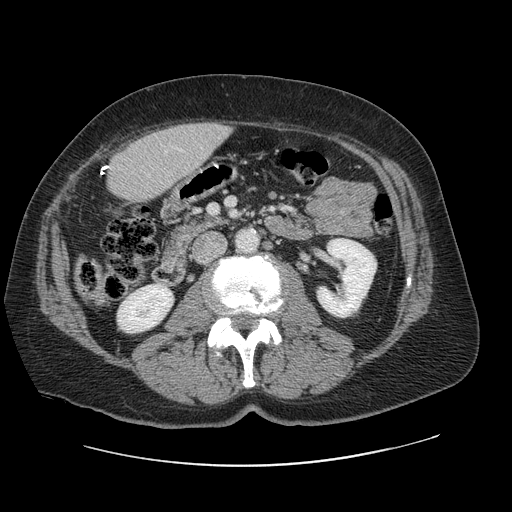
Contrast-enhanced abdominal CT, one axial slice; slice 23 of 138 in the series (ordered by position); intravenous contrast given; soft-tissue window (W 400 / L 40 HU); 512 × 512 image matrix. Male patient, age 71 years. Case-level facts recorded for this patient, not image findings: diagnosis: colorectal cancer liver metastases, imaged before liver resection; multiple liver metastases: no; largest metastasis: 3.3 cm; chemotherapy before resection: no.
Structures marked on this image (expert manual segmentation):
- liver: box from (x=108, y=123) to (x=229, y=204) px
- planned liver remnant (the part of the liver to remain after resection): (x=106, y=135)–(x=177, y=204)